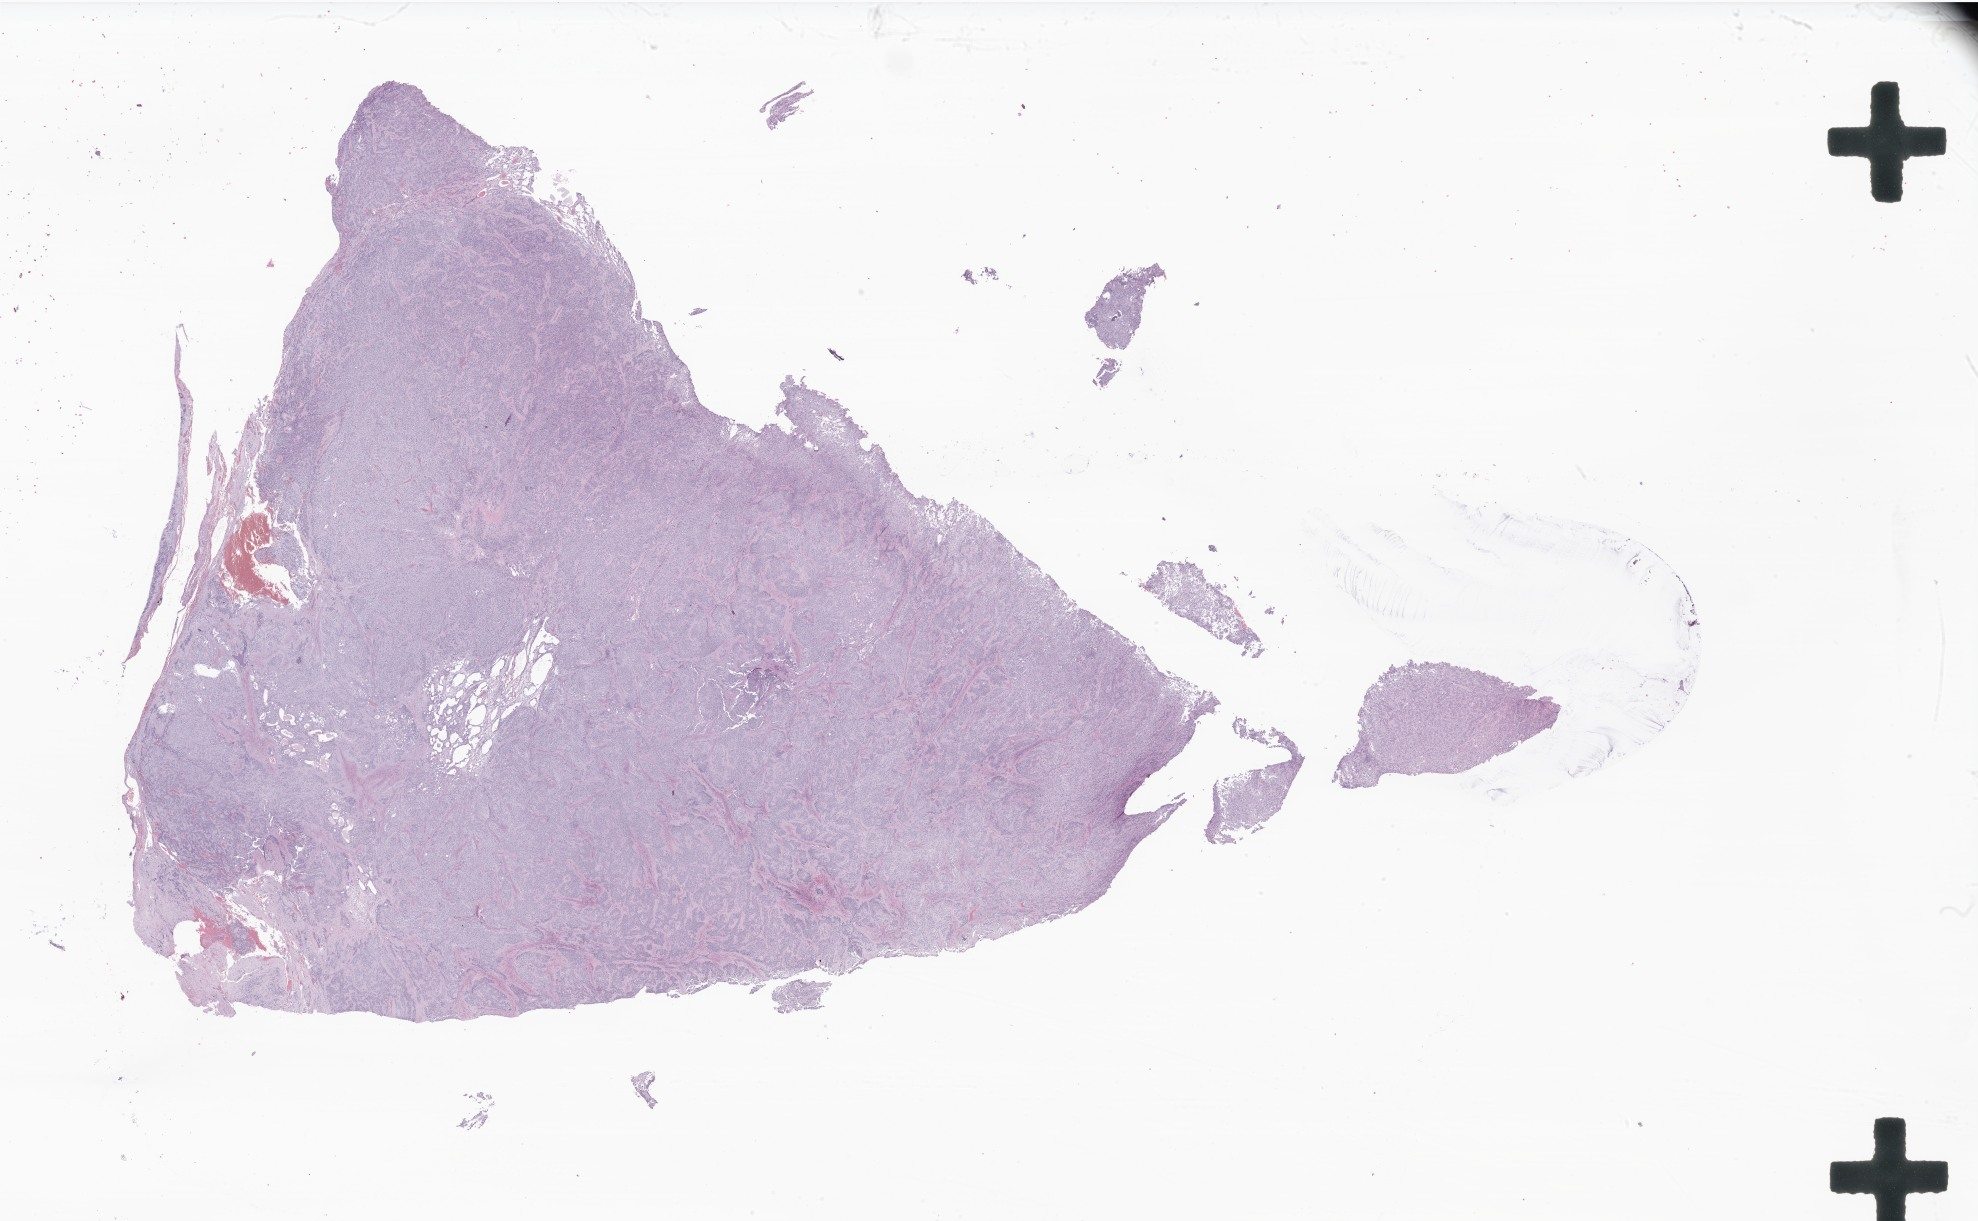
Hematoxylin and eosin (H&E) whole-slide image of tumor tissue from the brain — whole scanned area (about 33.4 x 20.6 mm) shown as a low-resolution overview, FFPE section. Patient: male, age 155 months (12 years 11 months).
Diagnosis: Glioma, malignant.